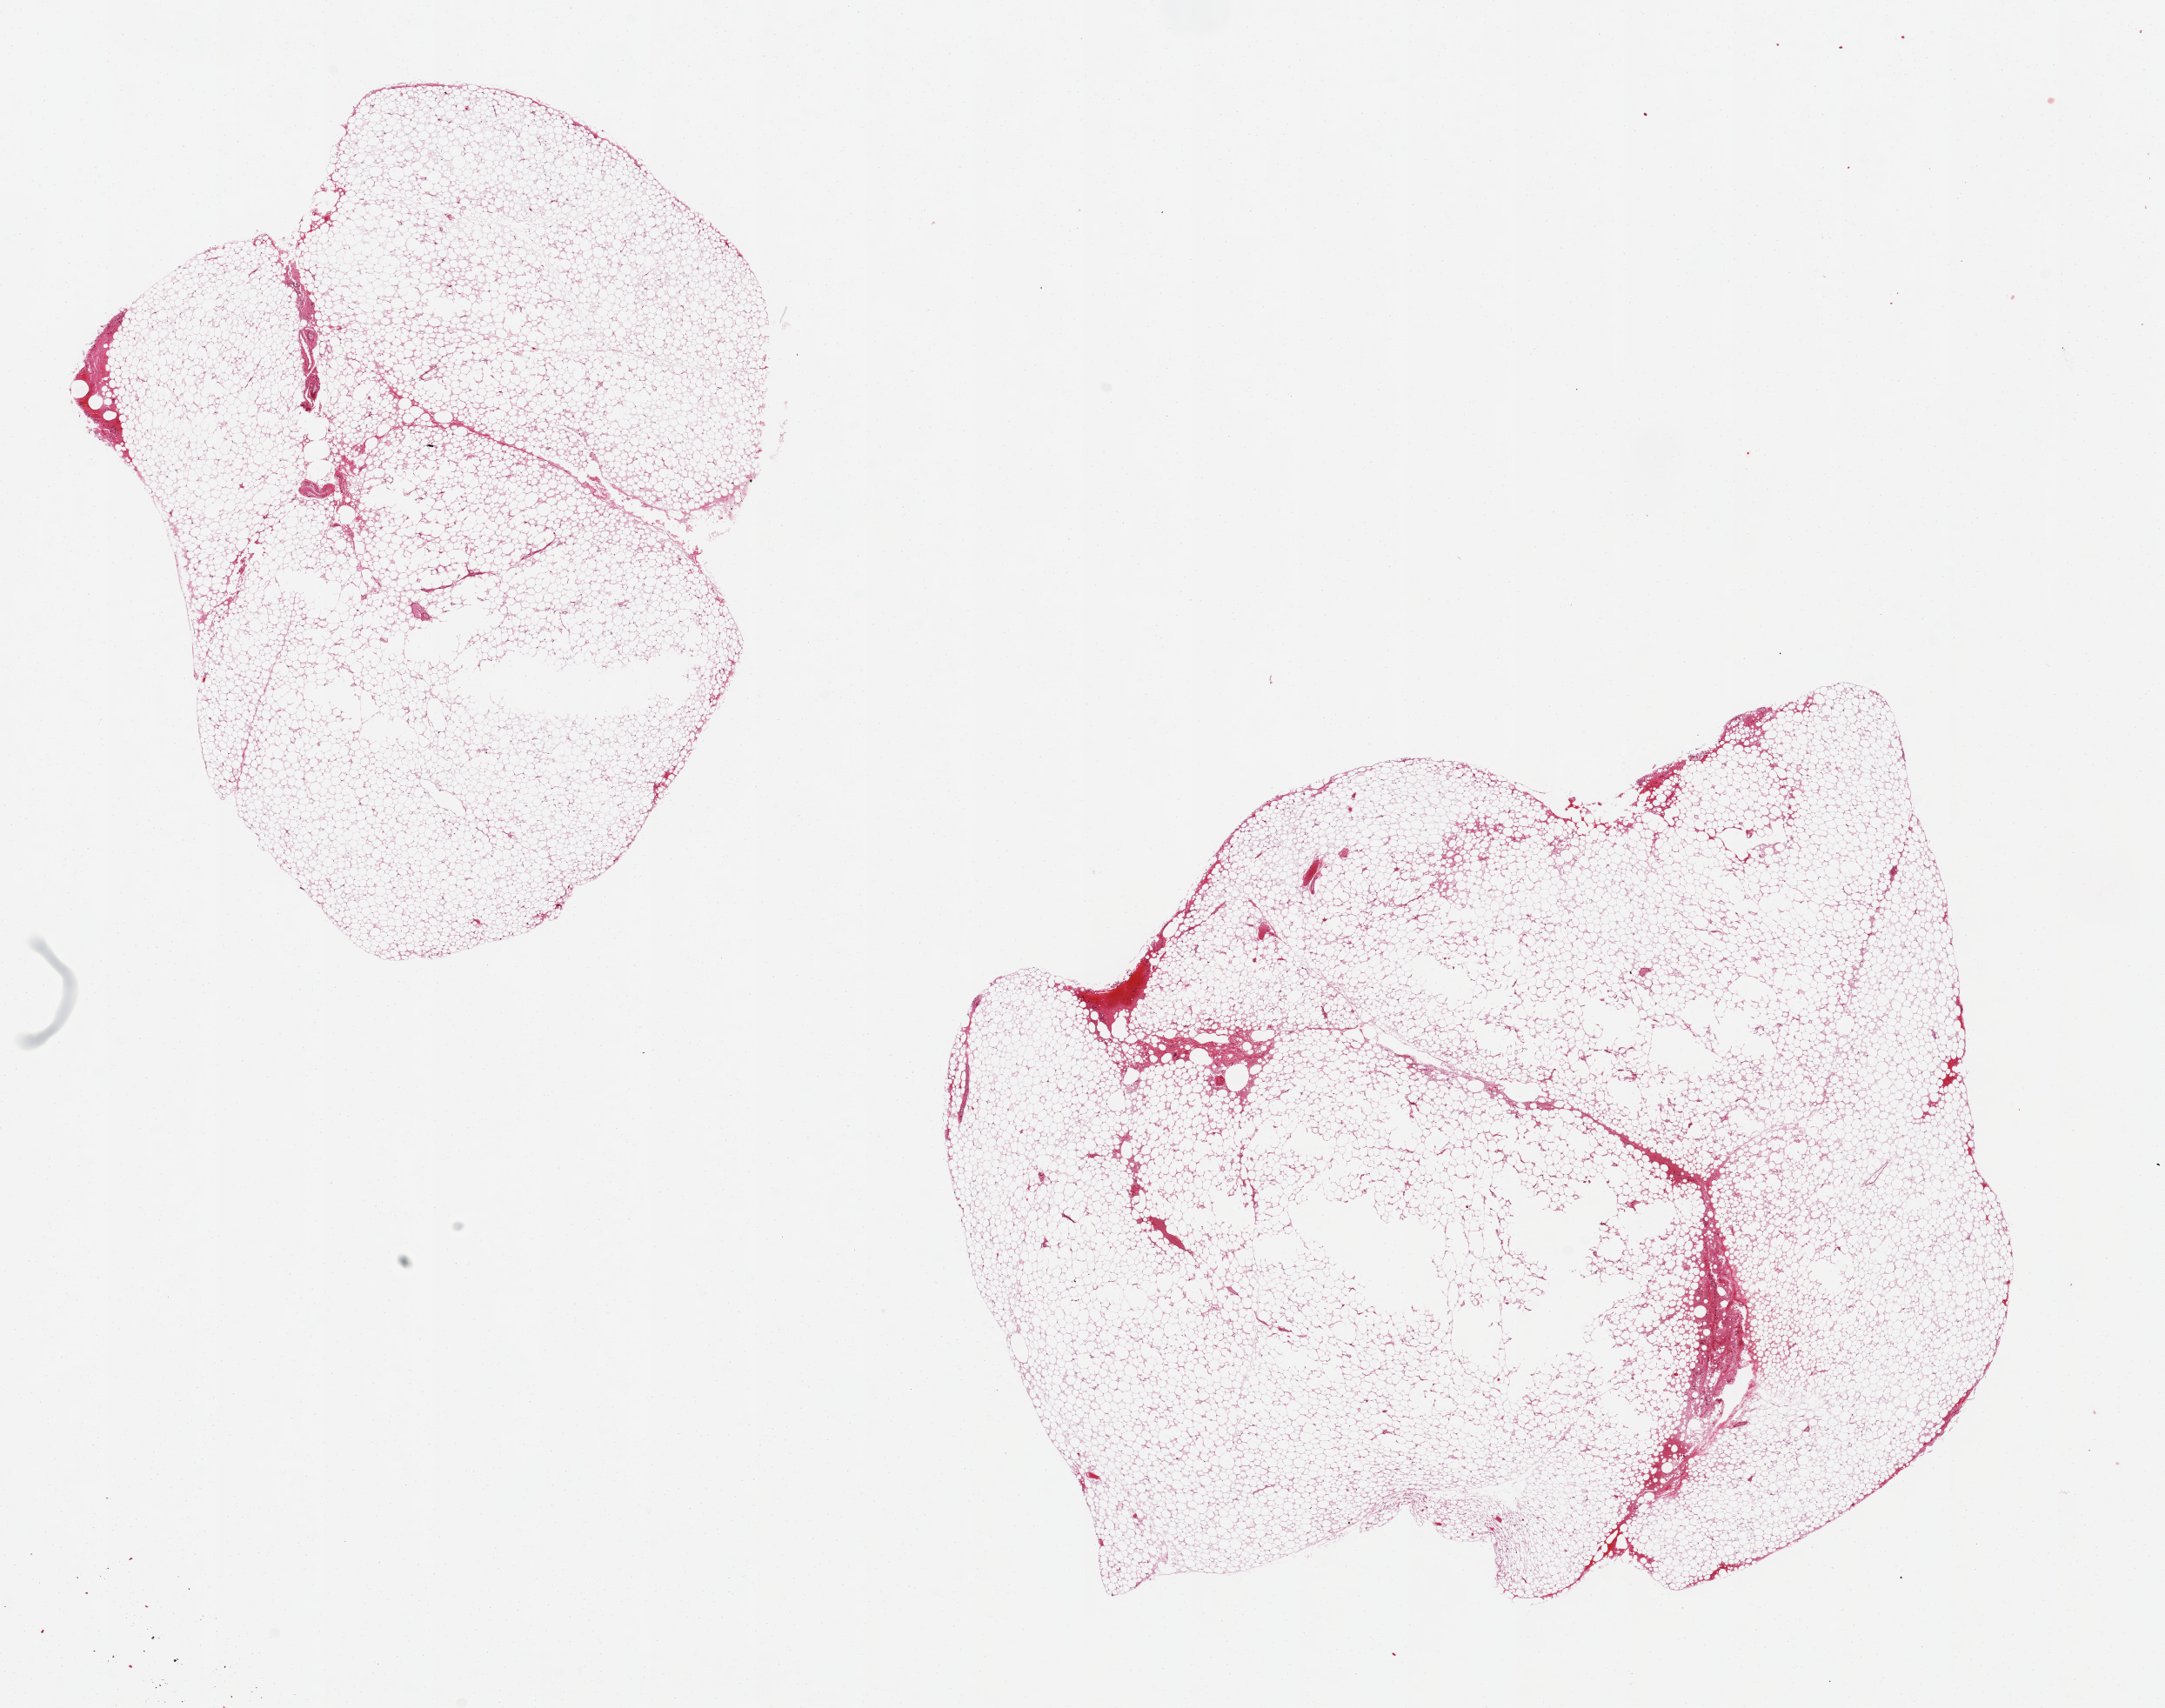
Whole-slide image, H&E stain — shown as a low-resolution overview of the whole scanned area (about 19.7 x 15.5 mm, acquisition: 20x scan). PAXgene-fixed paraffin-embedded (PFPE) section. Section of pancreas (target tissue). Tissue donor sample. Donor: female.
* reviewer comment on this tissue sample: 2 pieces, 9x8 & 7x7 mm; both pieces are all adipose; no pancreas